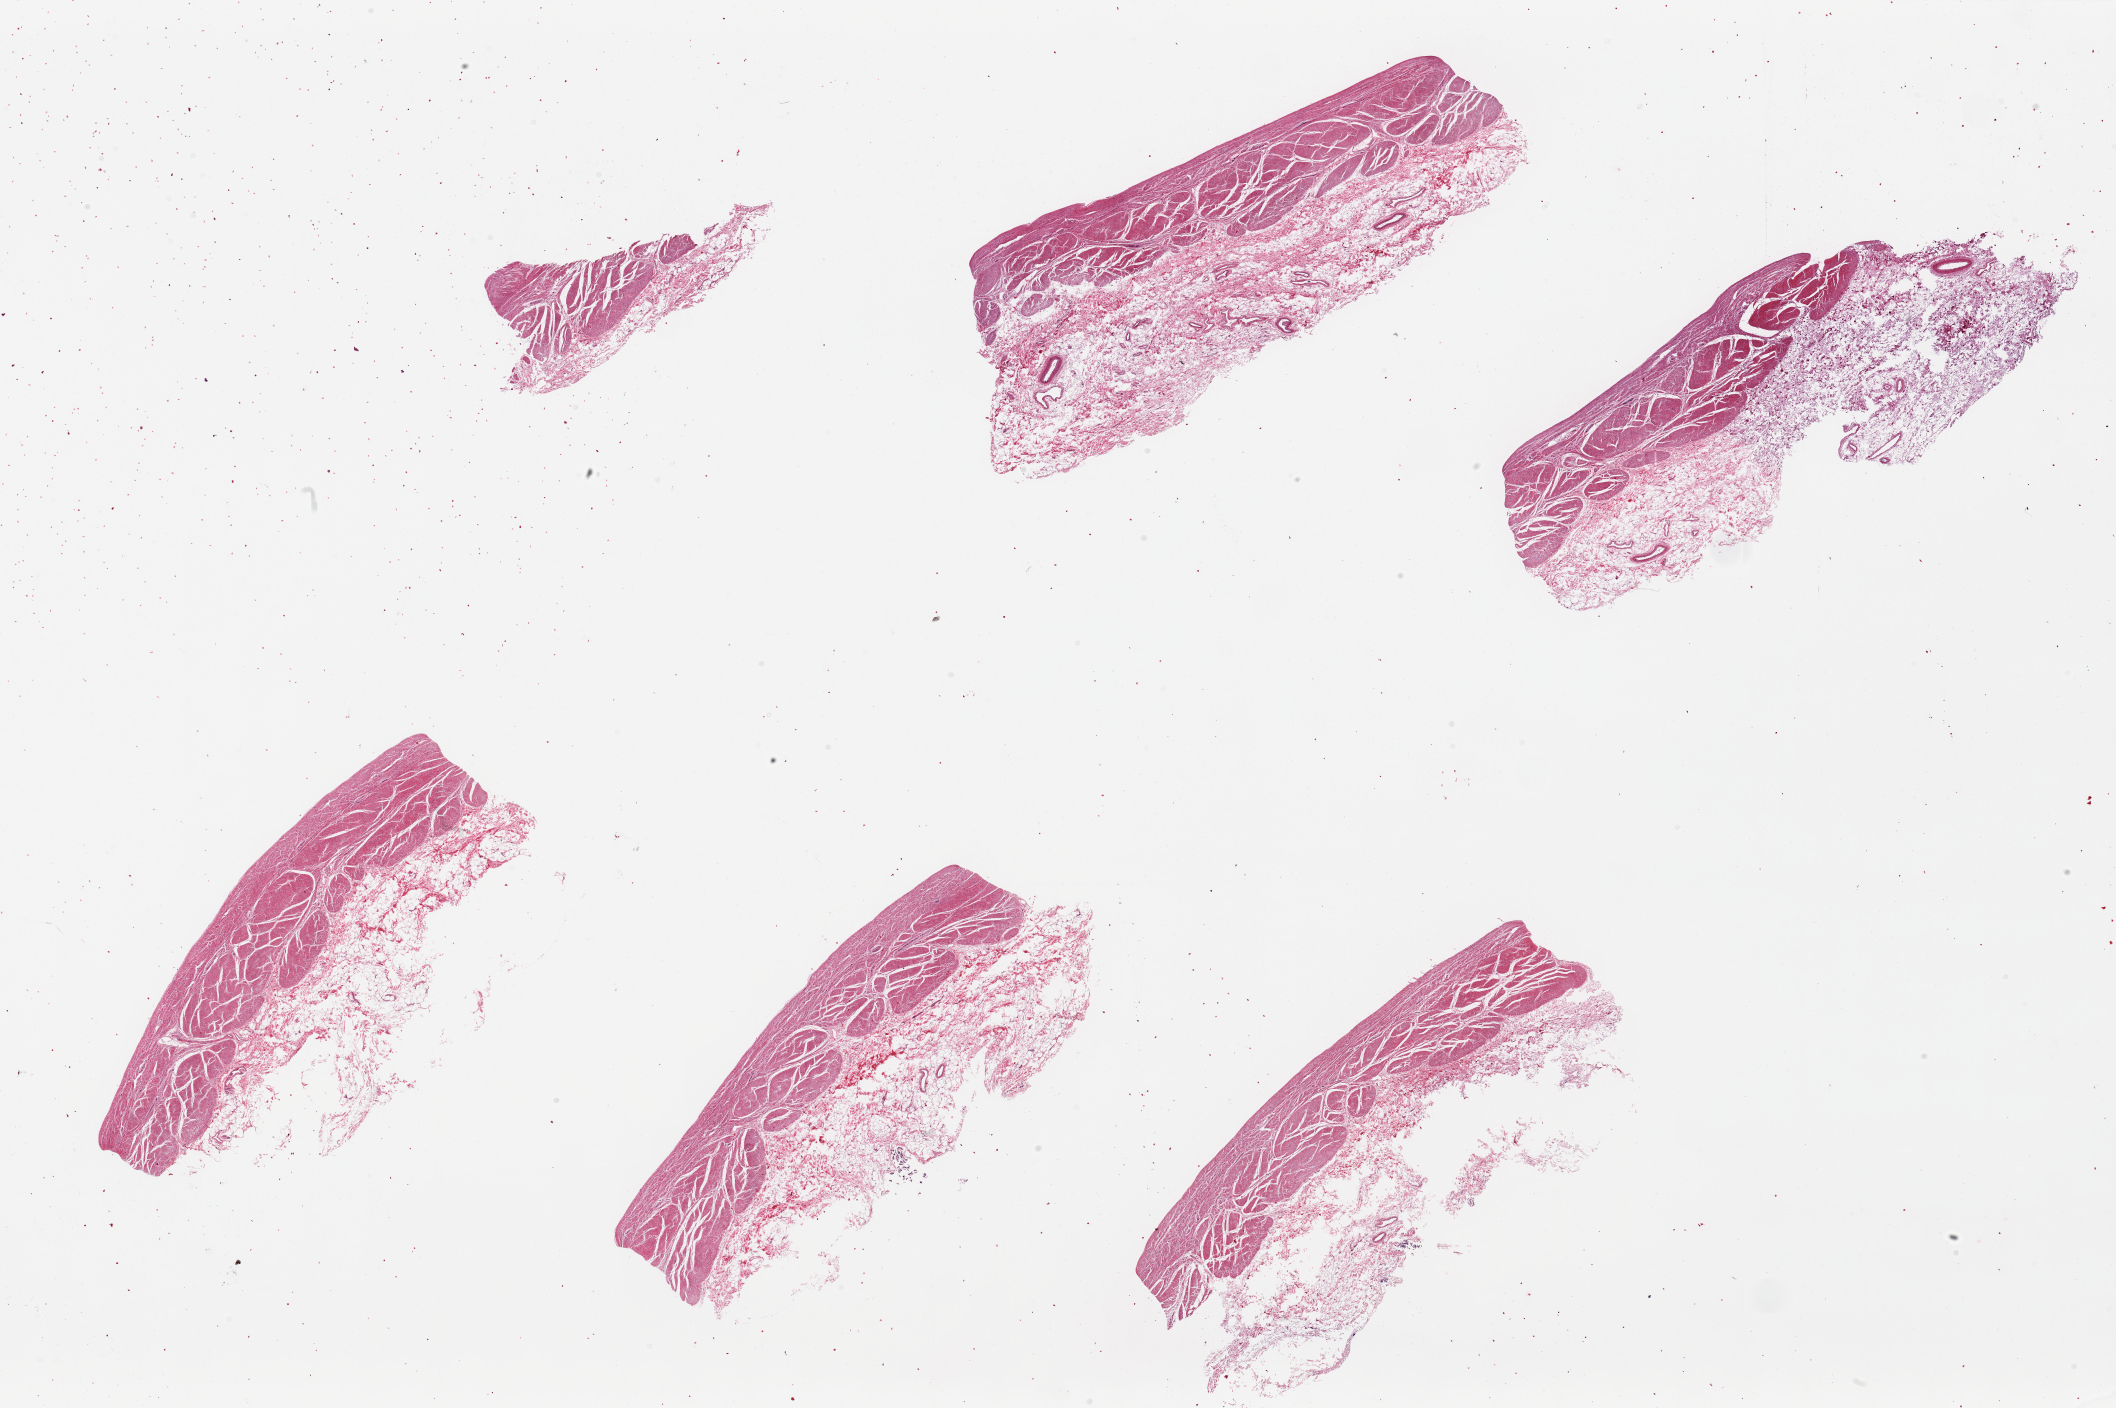
H&E whole-slide image, brightfield, whole scanned area (about 33.5 x 22.3 mm, acquisition: 20x scan) shown as a low-resolution overview. Donor sex: male.
* specimen: PAXgene-fixed paraffin-embedded (PFPE) section; sampled site (target tissue): stomach; donor tissue sample